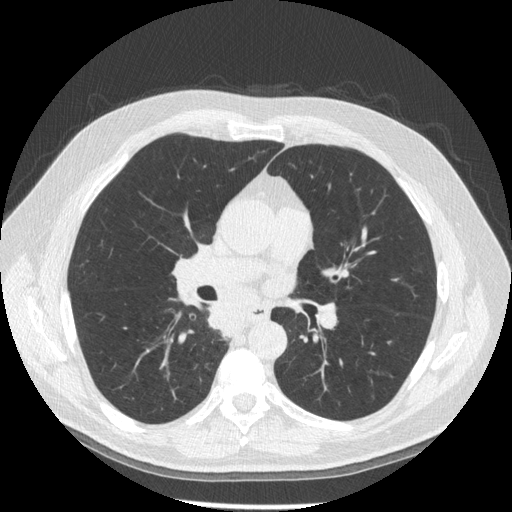
Low-dose screening chest CT, axial slice. Third screening round (two years after baseline). Lung window (W 1500 / L -600 HU). 1.25 mm slice thickness. Standard (soft-tissue) reconstruction kernel (STANDARD). Slice 81 of 181 in the series. Male, age 61 years at enrolment. Former smoker at enrolment.
Expert-annotated lung lesion, bounding box (x1, y1, x2, y2) in pixels: (206, 298, 256, 346). No non-calcified nodule or mass ≥4 mm was recorded by the screening reader at this exam. Participant outcome: lung cancer diagnosed 10 days after this screen — squamous cell carcinoma, keratinizing, NOS, right lower lobe, stage IIIB (AJCC 6th edition), 40 mm at pathology.